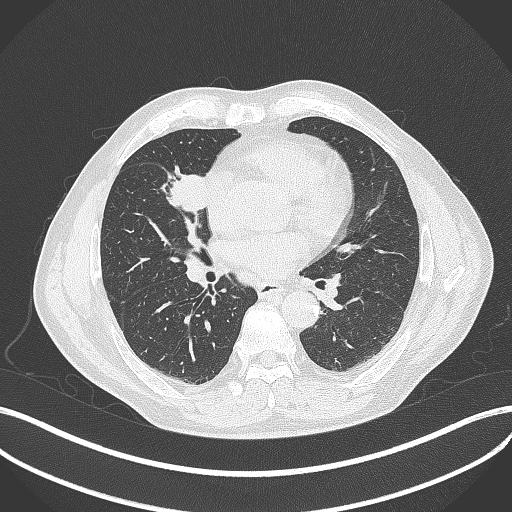
Chest CT, one axial slice. Slice 194 of 429 in the series (ordered by position). 120 kVp. Lung window (W 1500 / L -600 HU). 1 mm slice thickness. 512 × 512 image matrix. Patient: male, 61 years. Case-level facts recorded for this patient, not image findings: clinical TNM (as recorded): T2b N1 M0.
Annotated regions visible in this slice (bounding box drawn by a radiologist):
- lung tumour (recorded histology: squamous cell carcinoma): bounding box (x1, y1, x2, y2) in pixels: (159, 160, 213, 223)